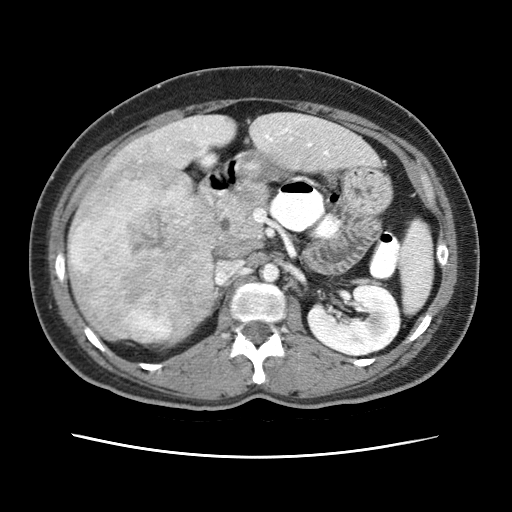
Contrast-enhanced abdominal CT (liver protocol), one axial slice. Slice 20 of 79 in the series (ordered by position). 120 kVp. Soft-tissue window (W 400 / L 40 HU). 2.5 mm slice thickness. 512 × 512 image matrix, field of view 340 × 340 mm. From the clinical record (not read from this slice): diagnosis: hepatocellular carcinoma (patient treated with transarterial chemoembolisation; whether this scan precedes or follows treatment is not stated here); TNM stage (as recorded): Stage-I; Child-Pugh class: A; tumour differentiation: moderately differentiated; tumour nodularity: uninodular.
Structures marked on this image (semi-automatically segmented with operator editing):
- abdominal aorta: box from (x=261, y=263) to (x=279, y=281) px
- liver parenchyma outside the tumour (the mass and vessels are separate outlines, so this box may not span the whole liver): (x=68, y=112)–(x=378, y=340)
- mass: (x=67, y=156)–(x=227, y=347)
- liver vessels: (x=194, y=125)–(x=328, y=155)